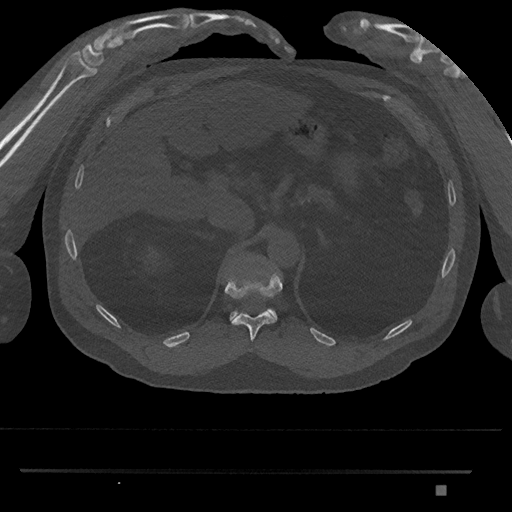
CT including the spine, one axial slice; position 931 of 1134 along the scan axis; reconstruction kernel Br40s/3; 120 kVp; bone window (W 1800 / L 400 HU); 0.5 mm slice thickness; 512 × 512 image matrix. Male patient, age 65 years. Case-level facts recorded for this patient, not image findings: primary cancer: prostate.
Structures marked on this image (semi-automatic segmentation, software-assisted and operator-edited):
- T11 vertebra: box from (x=225, y=274) to (x=282, y=342) px
- T12 vertebra: (x=229, y=308)–(x=278, y=321)